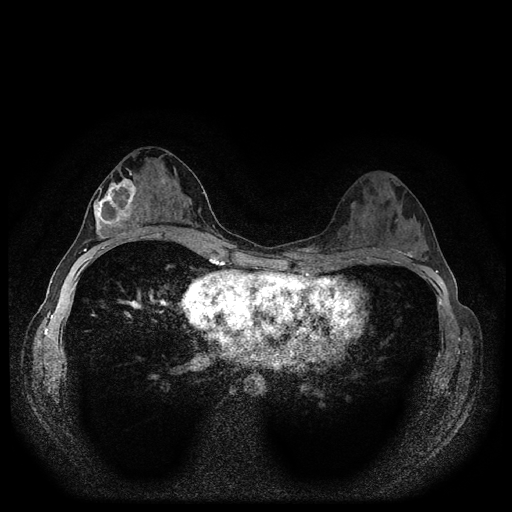
Breast MRI (dynamic contrast-enhanced, multi-phase), one axial slice. Position 57 of 116 along the scan axis. Dynamic contrast-enhanced series, time point 2 of 5 at this slice position (early post-contrast). 1.5 T. TE 2.7 ms, TR 5.4 ms. 2 mm slice thickness. 512 × 512 image matrix, field of view 320 × 320 mm. Female patient, age 29 years.
Structures marked on this image (semi-automatically segmented with operator editing):
- breast lesion (labelled 'tumour' in the annotation; benign lesions carry a separate 'benign' label): bounding box [x1, y1, x2, y2] px = [91, 174, 139, 240]